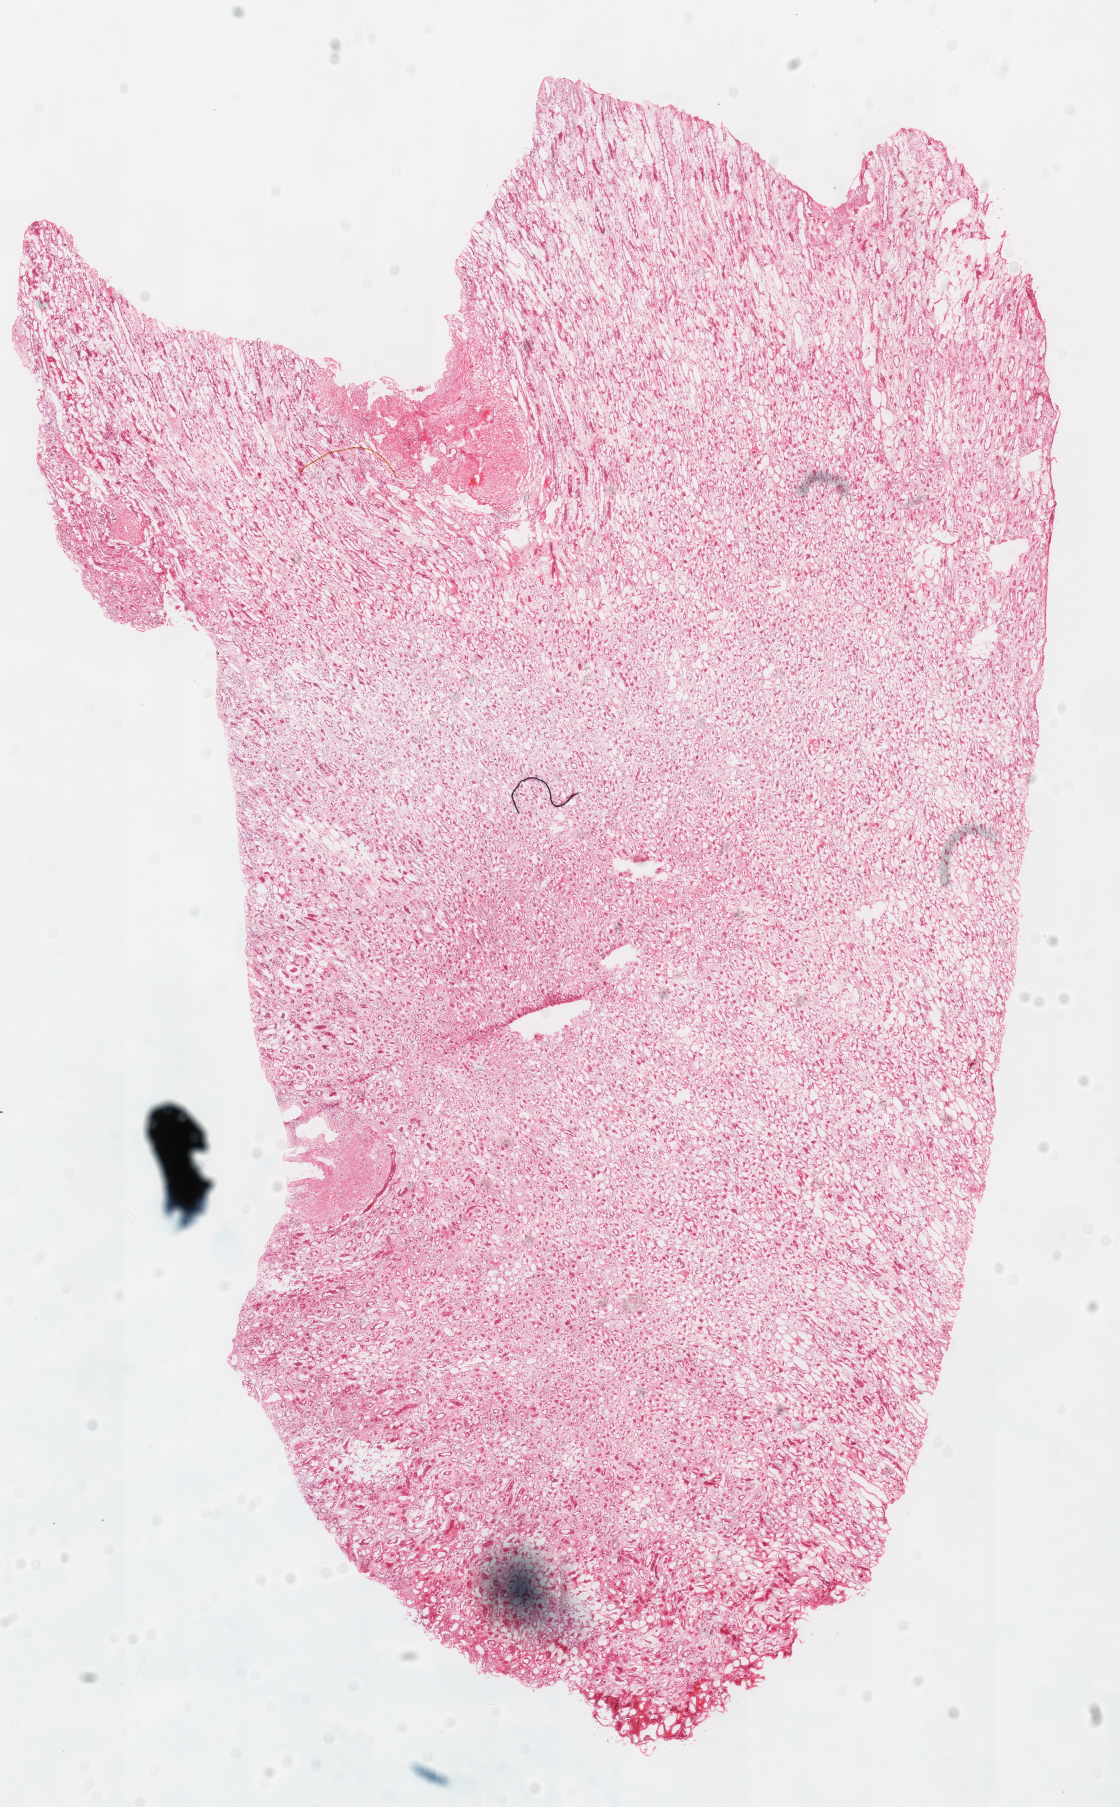
Hematoxylin and eosin (H&E) stained whole-slide image — a low-resolution overview of the entire scanned area, about 8.8 x 14.2 mm (acquisition: 40x scan); frozen section from the top of the tissue portion; sample: solid tissue normal (non-tumour tissue), kidney. Patient: male, age at initial diagnosis 54 years. Infiltration values recorded for this section: lymphocyte infiltration 0%, monocyte infiltration 0%, neutrophil infiltration 0%.
* this section: solid tissue normal sample (biorepository sample class)
* patient diagnosis: Renal cell carcinoma, chromophobe type